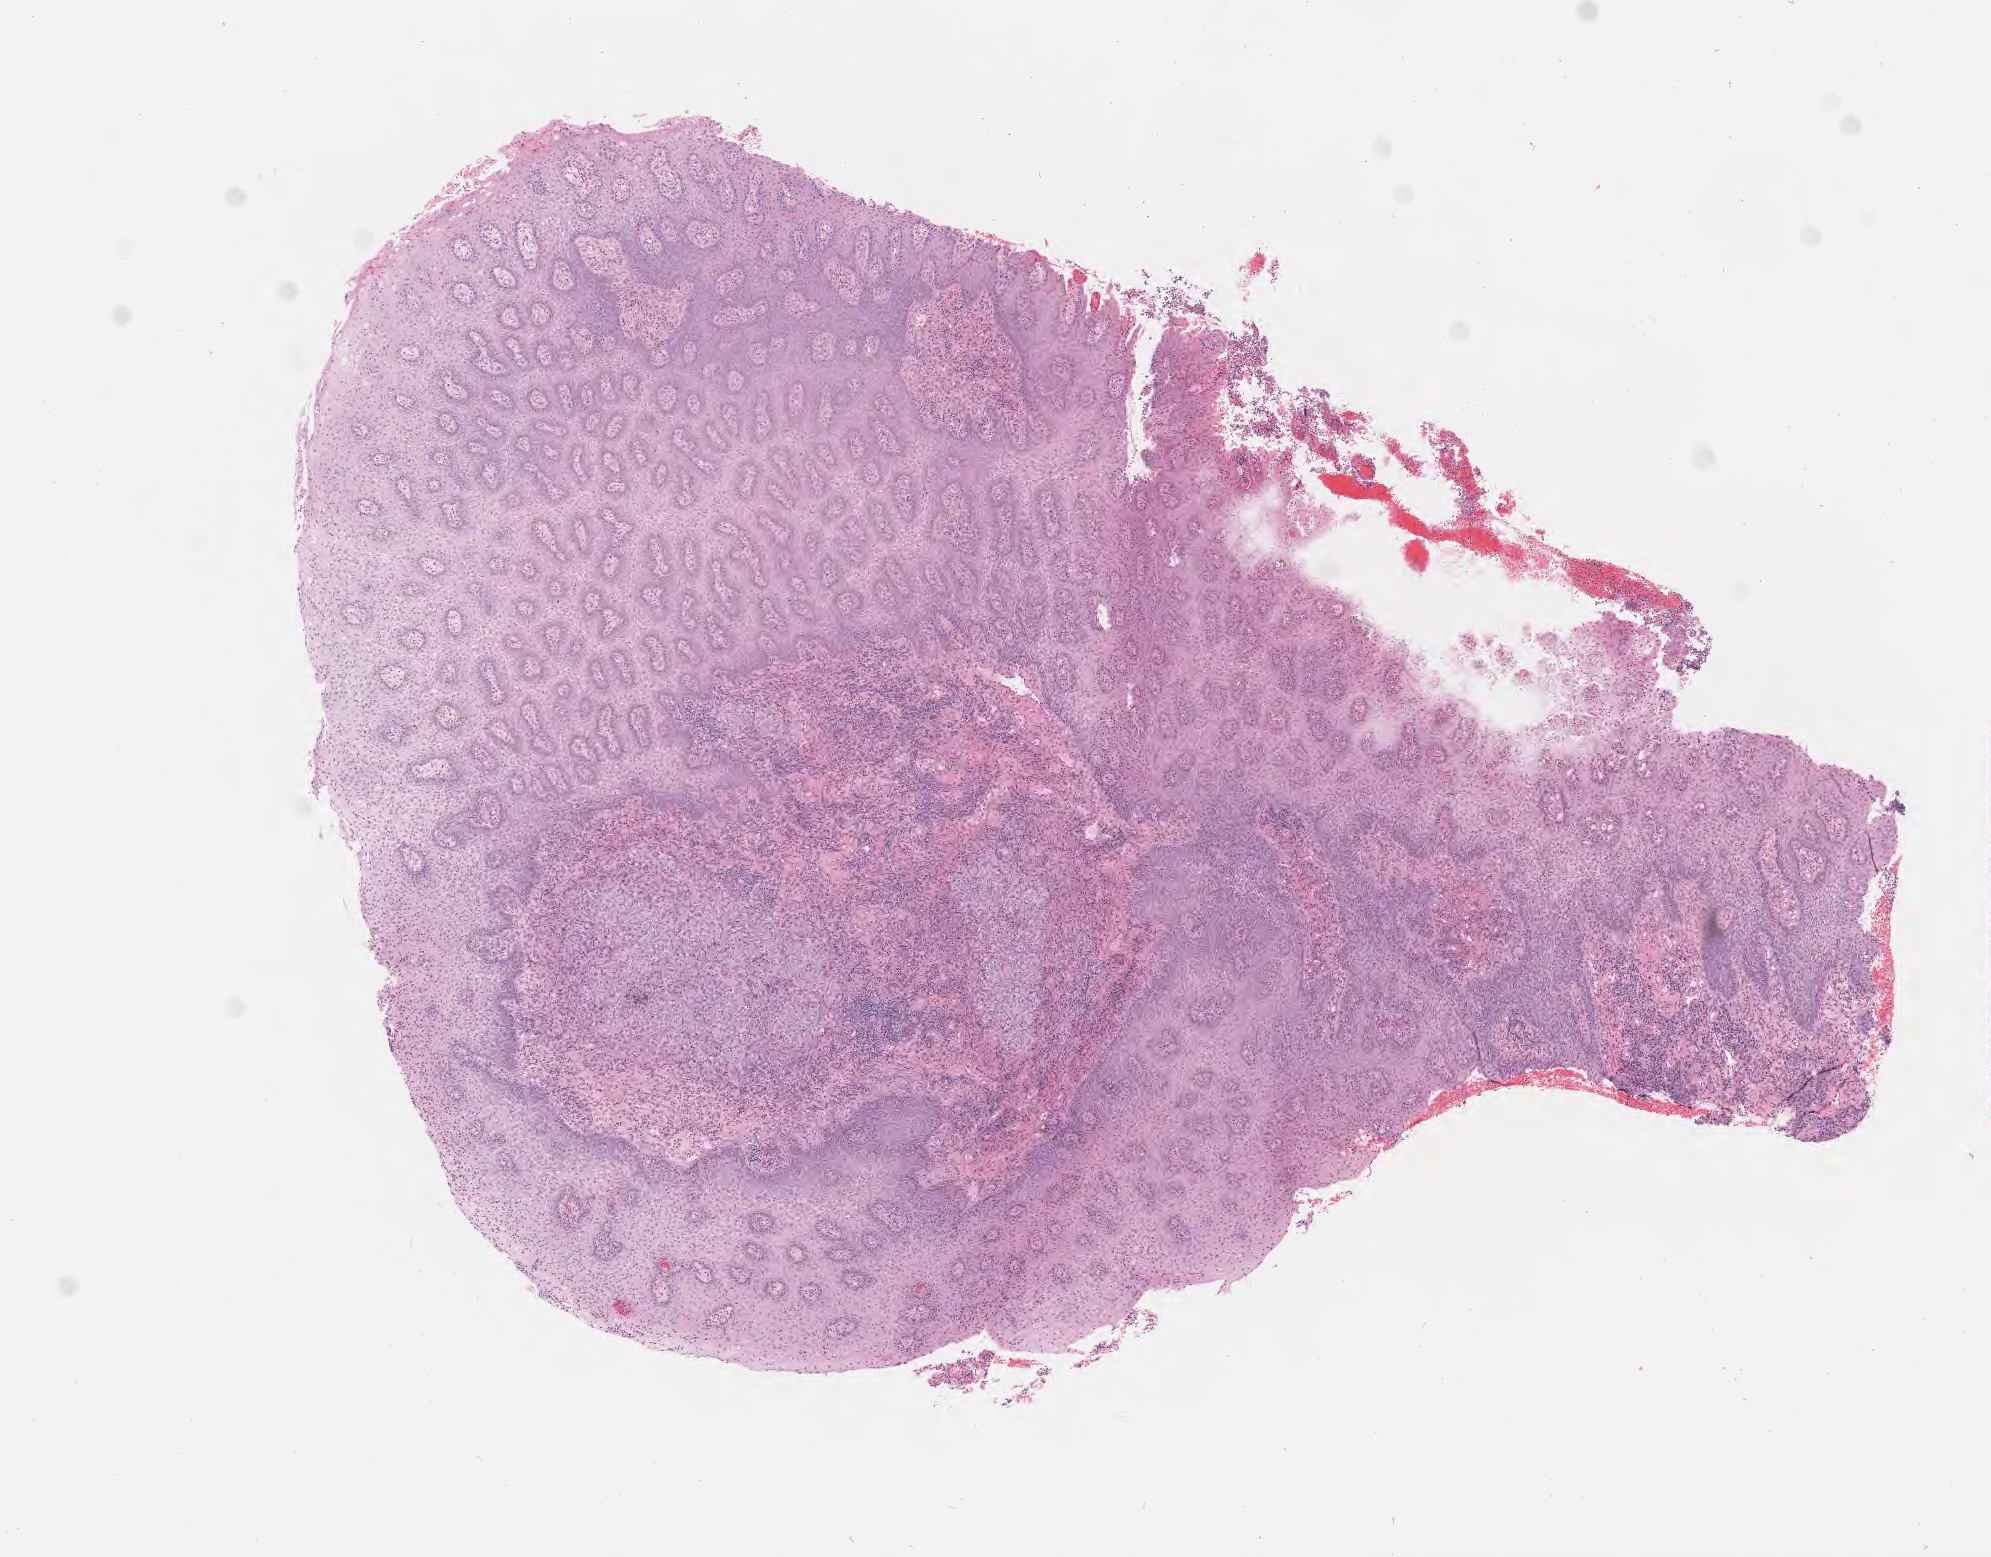
Hematoxylin and eosin (H&E) whole-slide image — a low-resolution overview of the entire scanned area, about 8.1 x 6.3 mm, specimen: tumor tissue, anatomic site: cervix. Female patient, age 32 years.
Histologic diagnosis: Squamous cell carcinoma, large cell, nonkeratinizing, NOS.